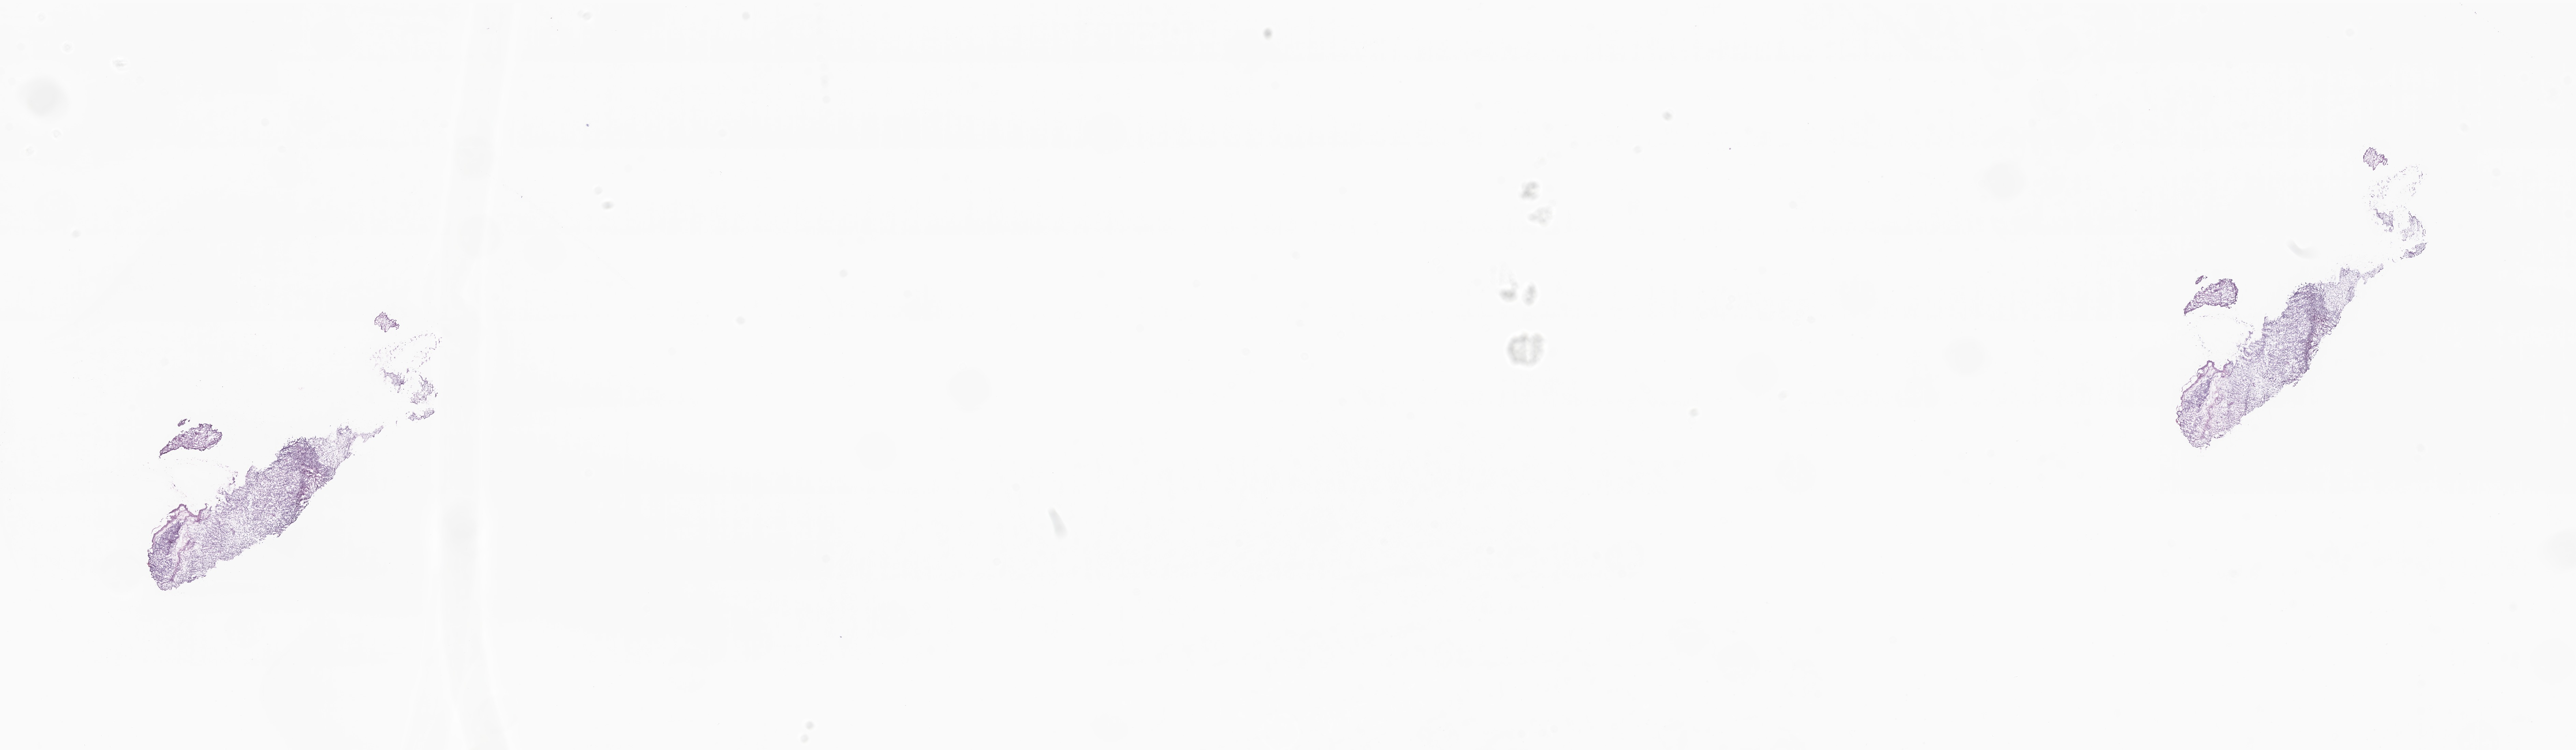
Digitized hematoxylin and eosin (H&E)-stained section of tumor tissue from the abdomen — shown as a low-resolution overview of the whole scanned area (about 31.8 x 9.3 mm); cryosection (OCT / tissue freezing medium). Male patient, age 75 months (6 years 3 months).
- diagnosis (ICD-O-3 morphology term): Rhabdomyosarcoma, NOS